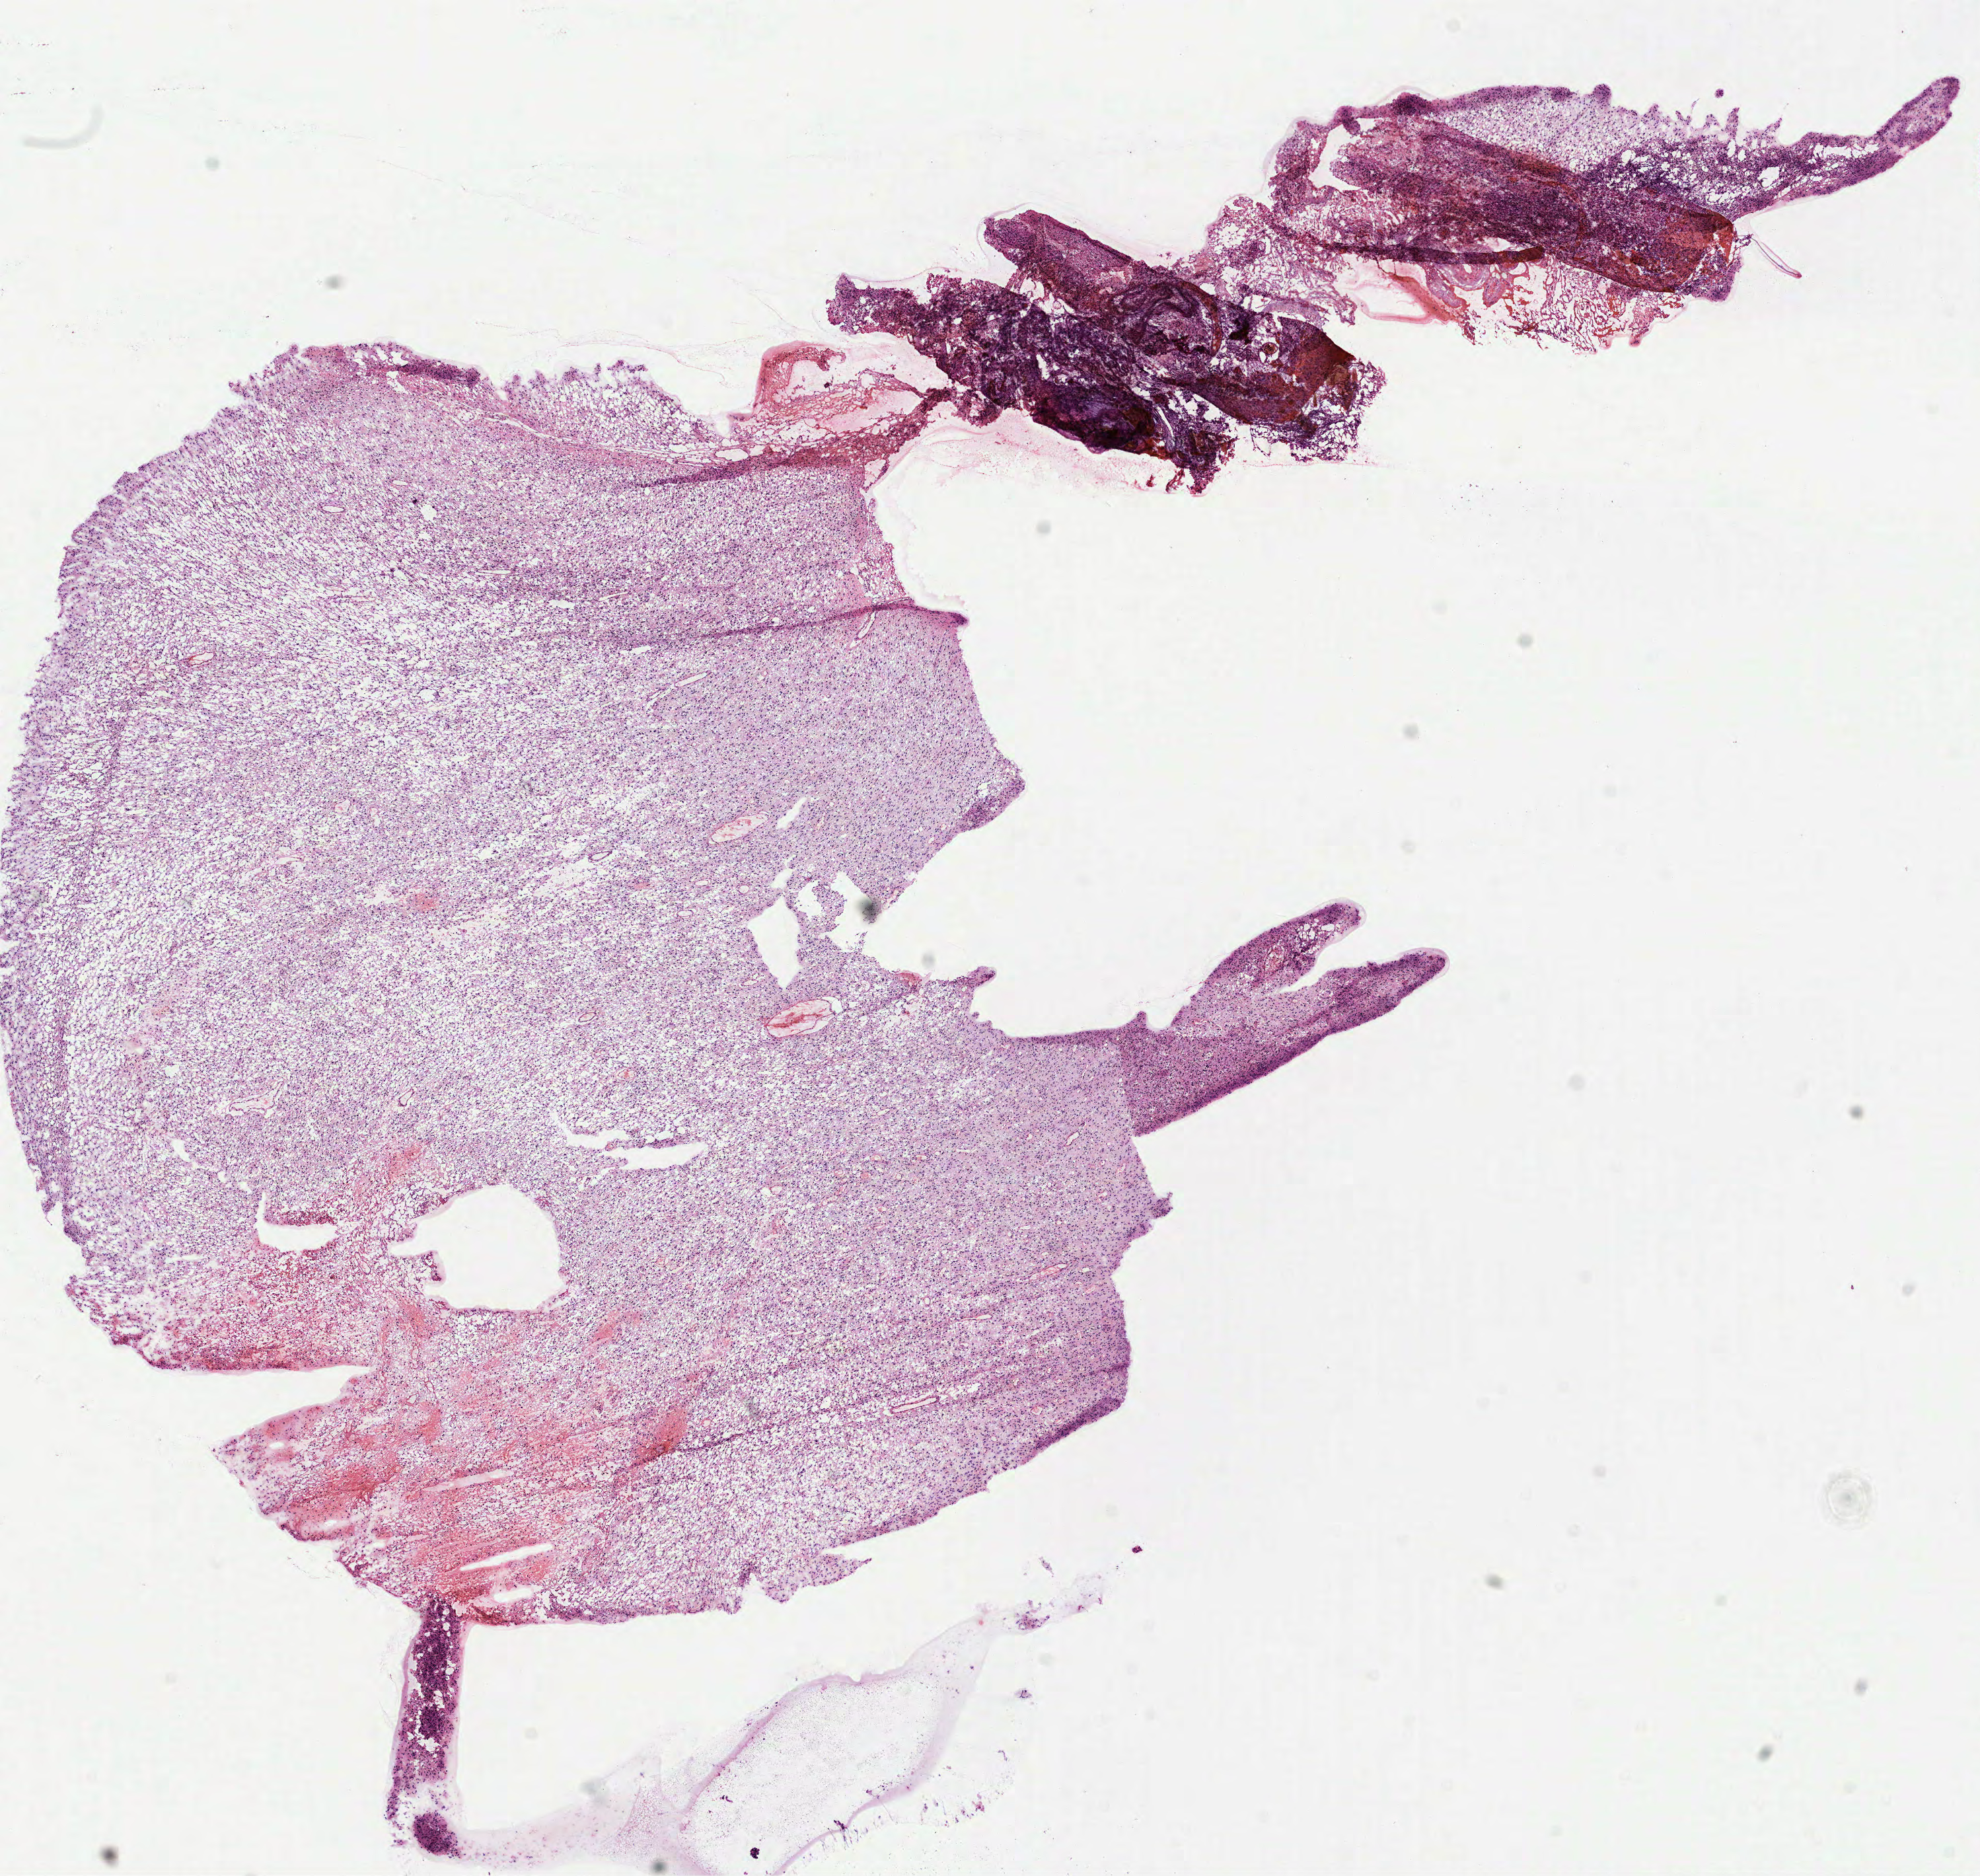
Hematoxylin and eosin (H&E) stained whole-slide image, low-resolution overview of the scanned area, about 12.1 x 11.4 mm. Frozen section from the top of the tissue portion. Primary tumour sample from the brain. Male patient; age at initial diagnosis 14 years. Histologic grade: G2 (moderately differentiated). Composition of this section per pathologist review: tumour cells 100%, tumour nuclei 80%, normal cells 0%, stromal cells 0%, necrosis 0%.
* pathologic diagnosis: Mixed glioma (cerebrum)